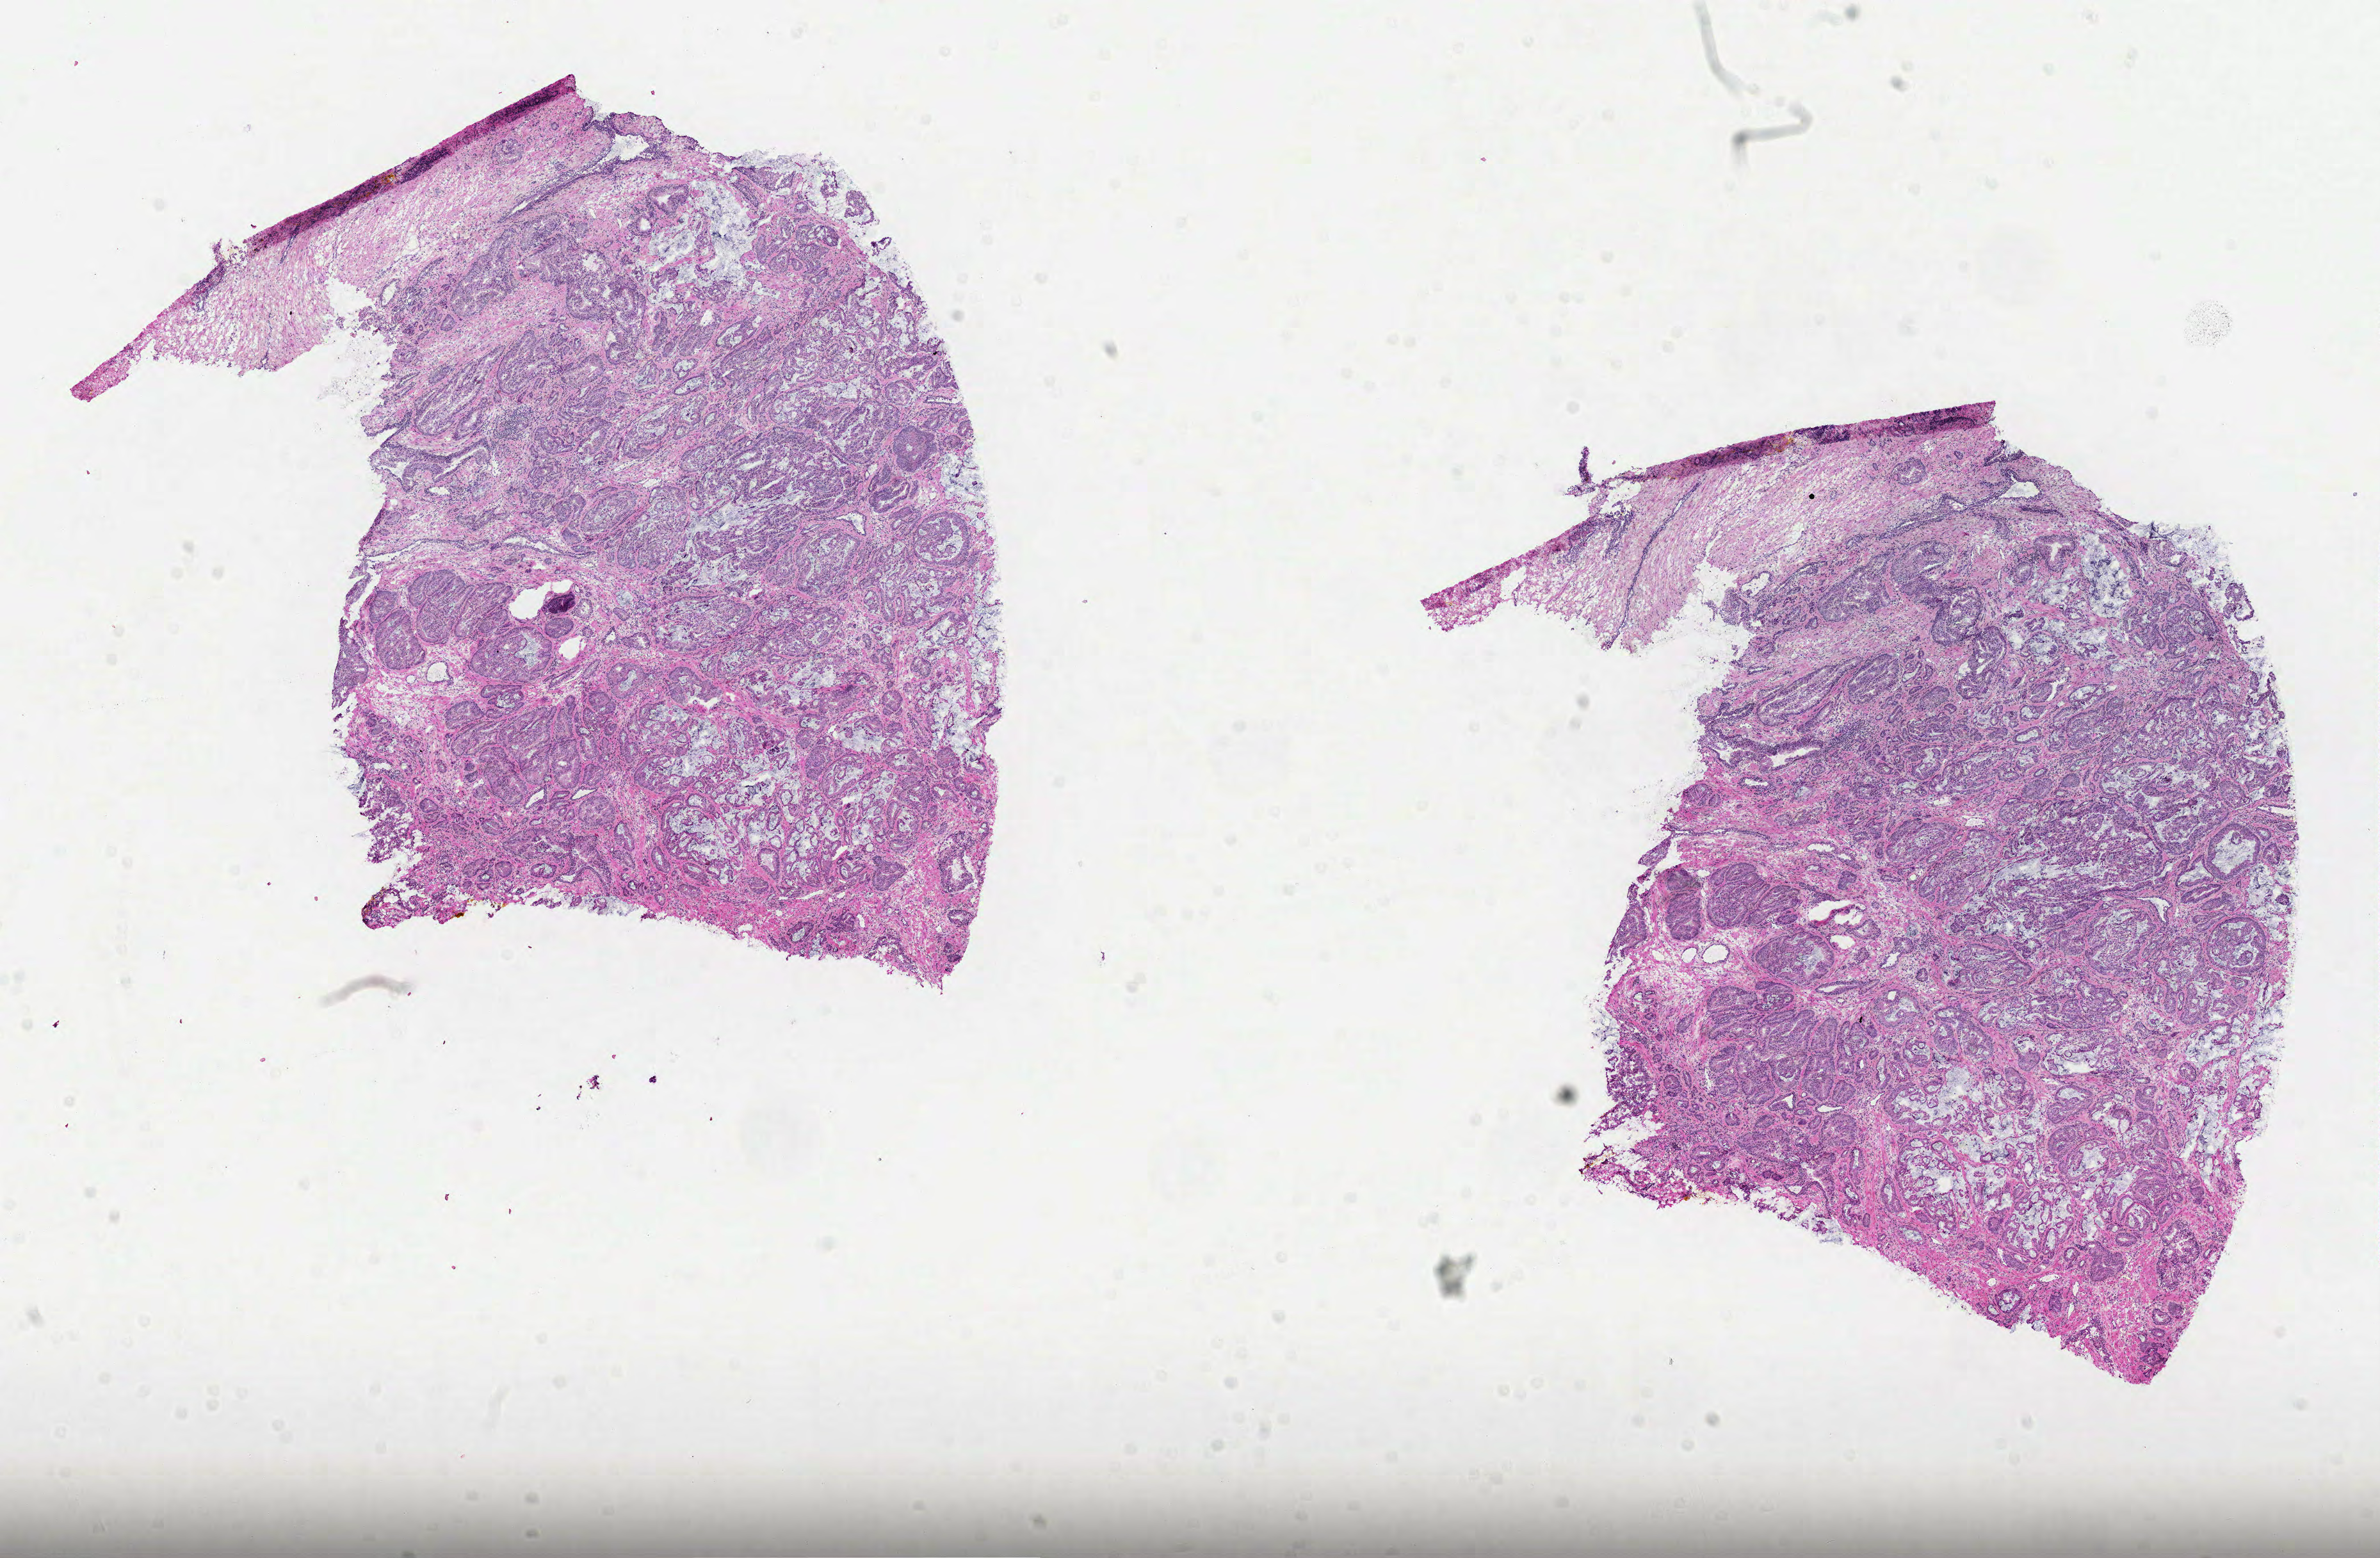
Whole-slide histology image, H&E-stained — low-resolution overview of the scanned area, about 15.0 x 9.8 mm (slide scanned at 40x); formalin-fixed paraffin-embedded (FFPE) diagnostic section; primary tumour sample from the prostate. Male patient; age at initial diagnosis 64 years. Gleason score: 7 (4+3).
Lymph nodes positive (case pathology): 0 of 3 examined. Histologic diagnosis: Acinar cell carcinoma (prostate gland).